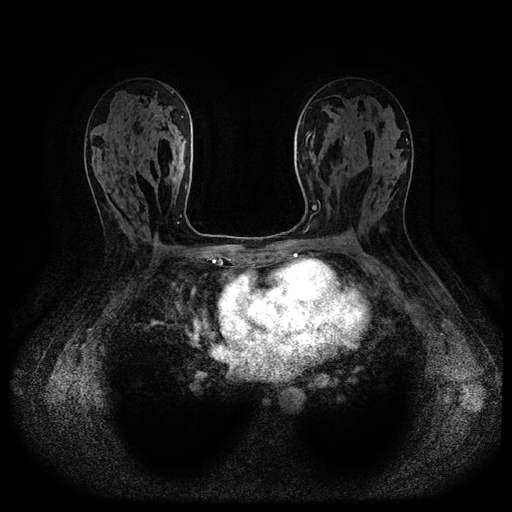
Breast MRI (dynamic contrast-enhanced, multi-phase), one axial slice; slice 62 of 116 in the series (ordered by position); dynamic contrast-enhanced series, time point 2 of 5 at this slice position (early post-contrast); 1.5 T; TE 2.6 ms, TR 5.3 ms; 512 × 512 image matrix. Patient: female, 54 years.
Outlined on this slice (semi-automatically segmented with operator editing):
- breast lesion (labelled benign in the annotation): box from (x=345, y=136) to (x=349, y=145) px